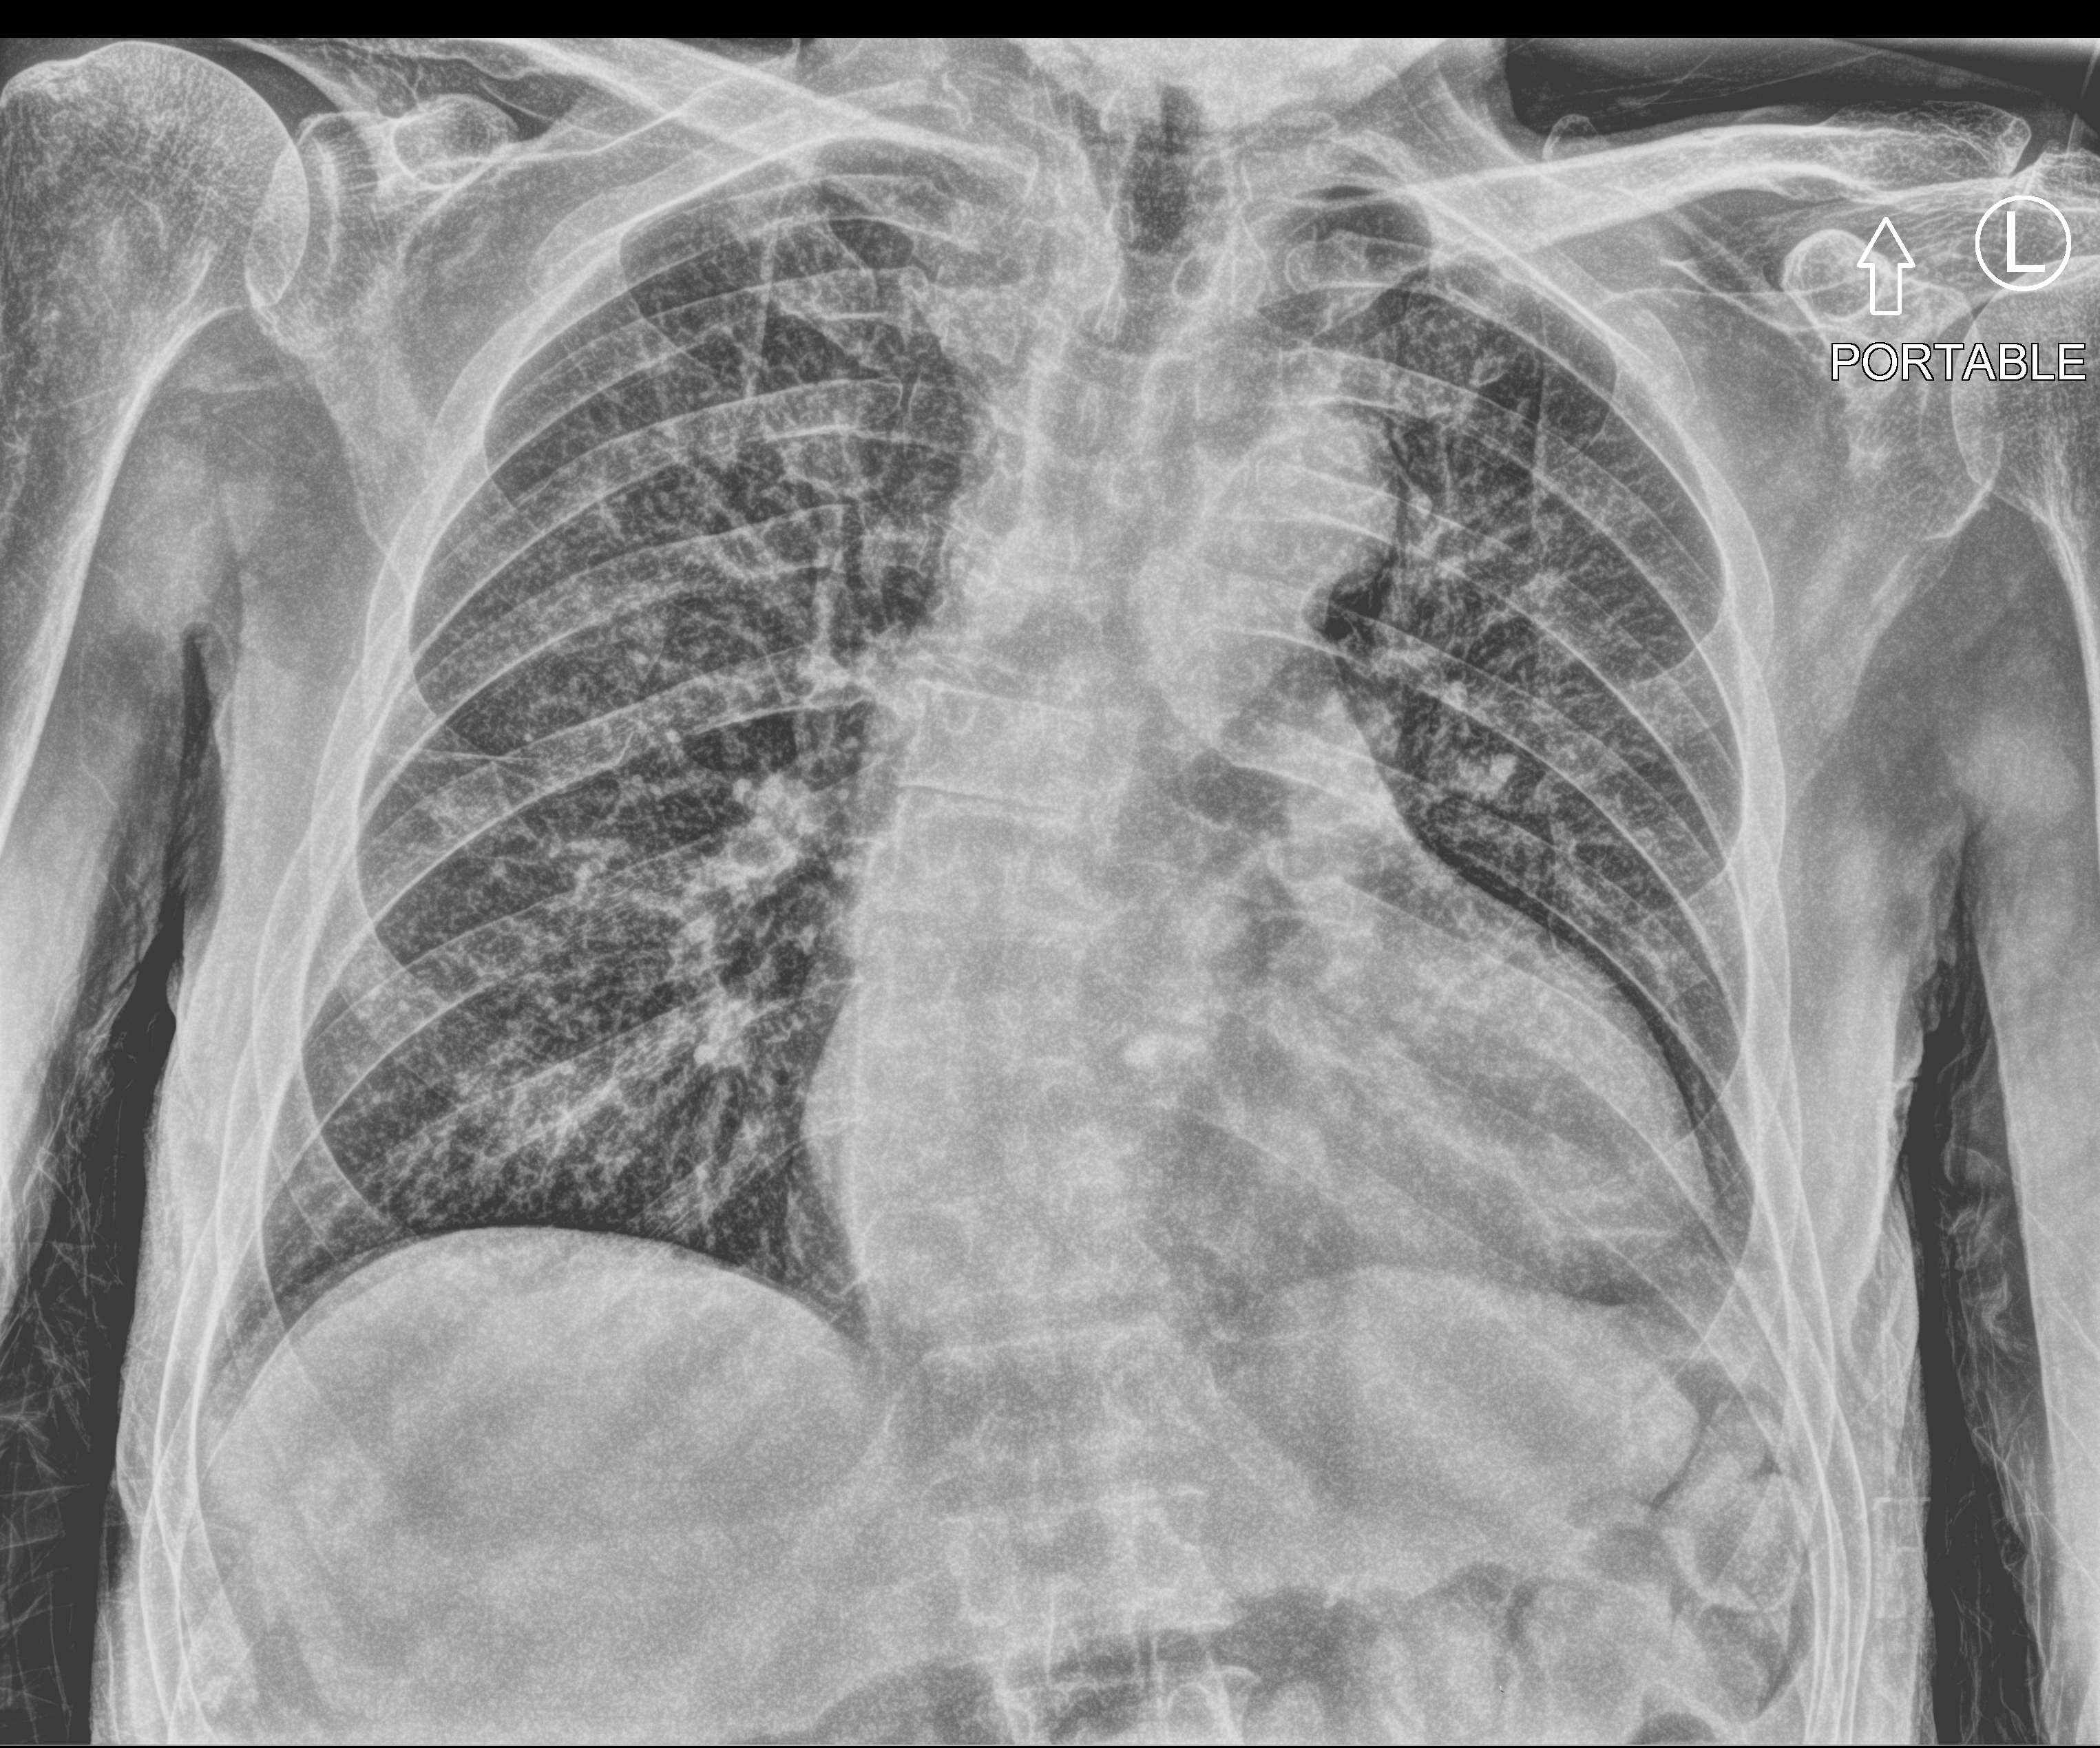
Portable chest radiograph; anteroposterior (AP) projection. Patient hospitalised with COVID-19; male, aged 75–90 years.
From the hospital-stay record, not from the radiograph (when in the stay this image was taken is not recorded): other chronic lung disease (admission record): no.